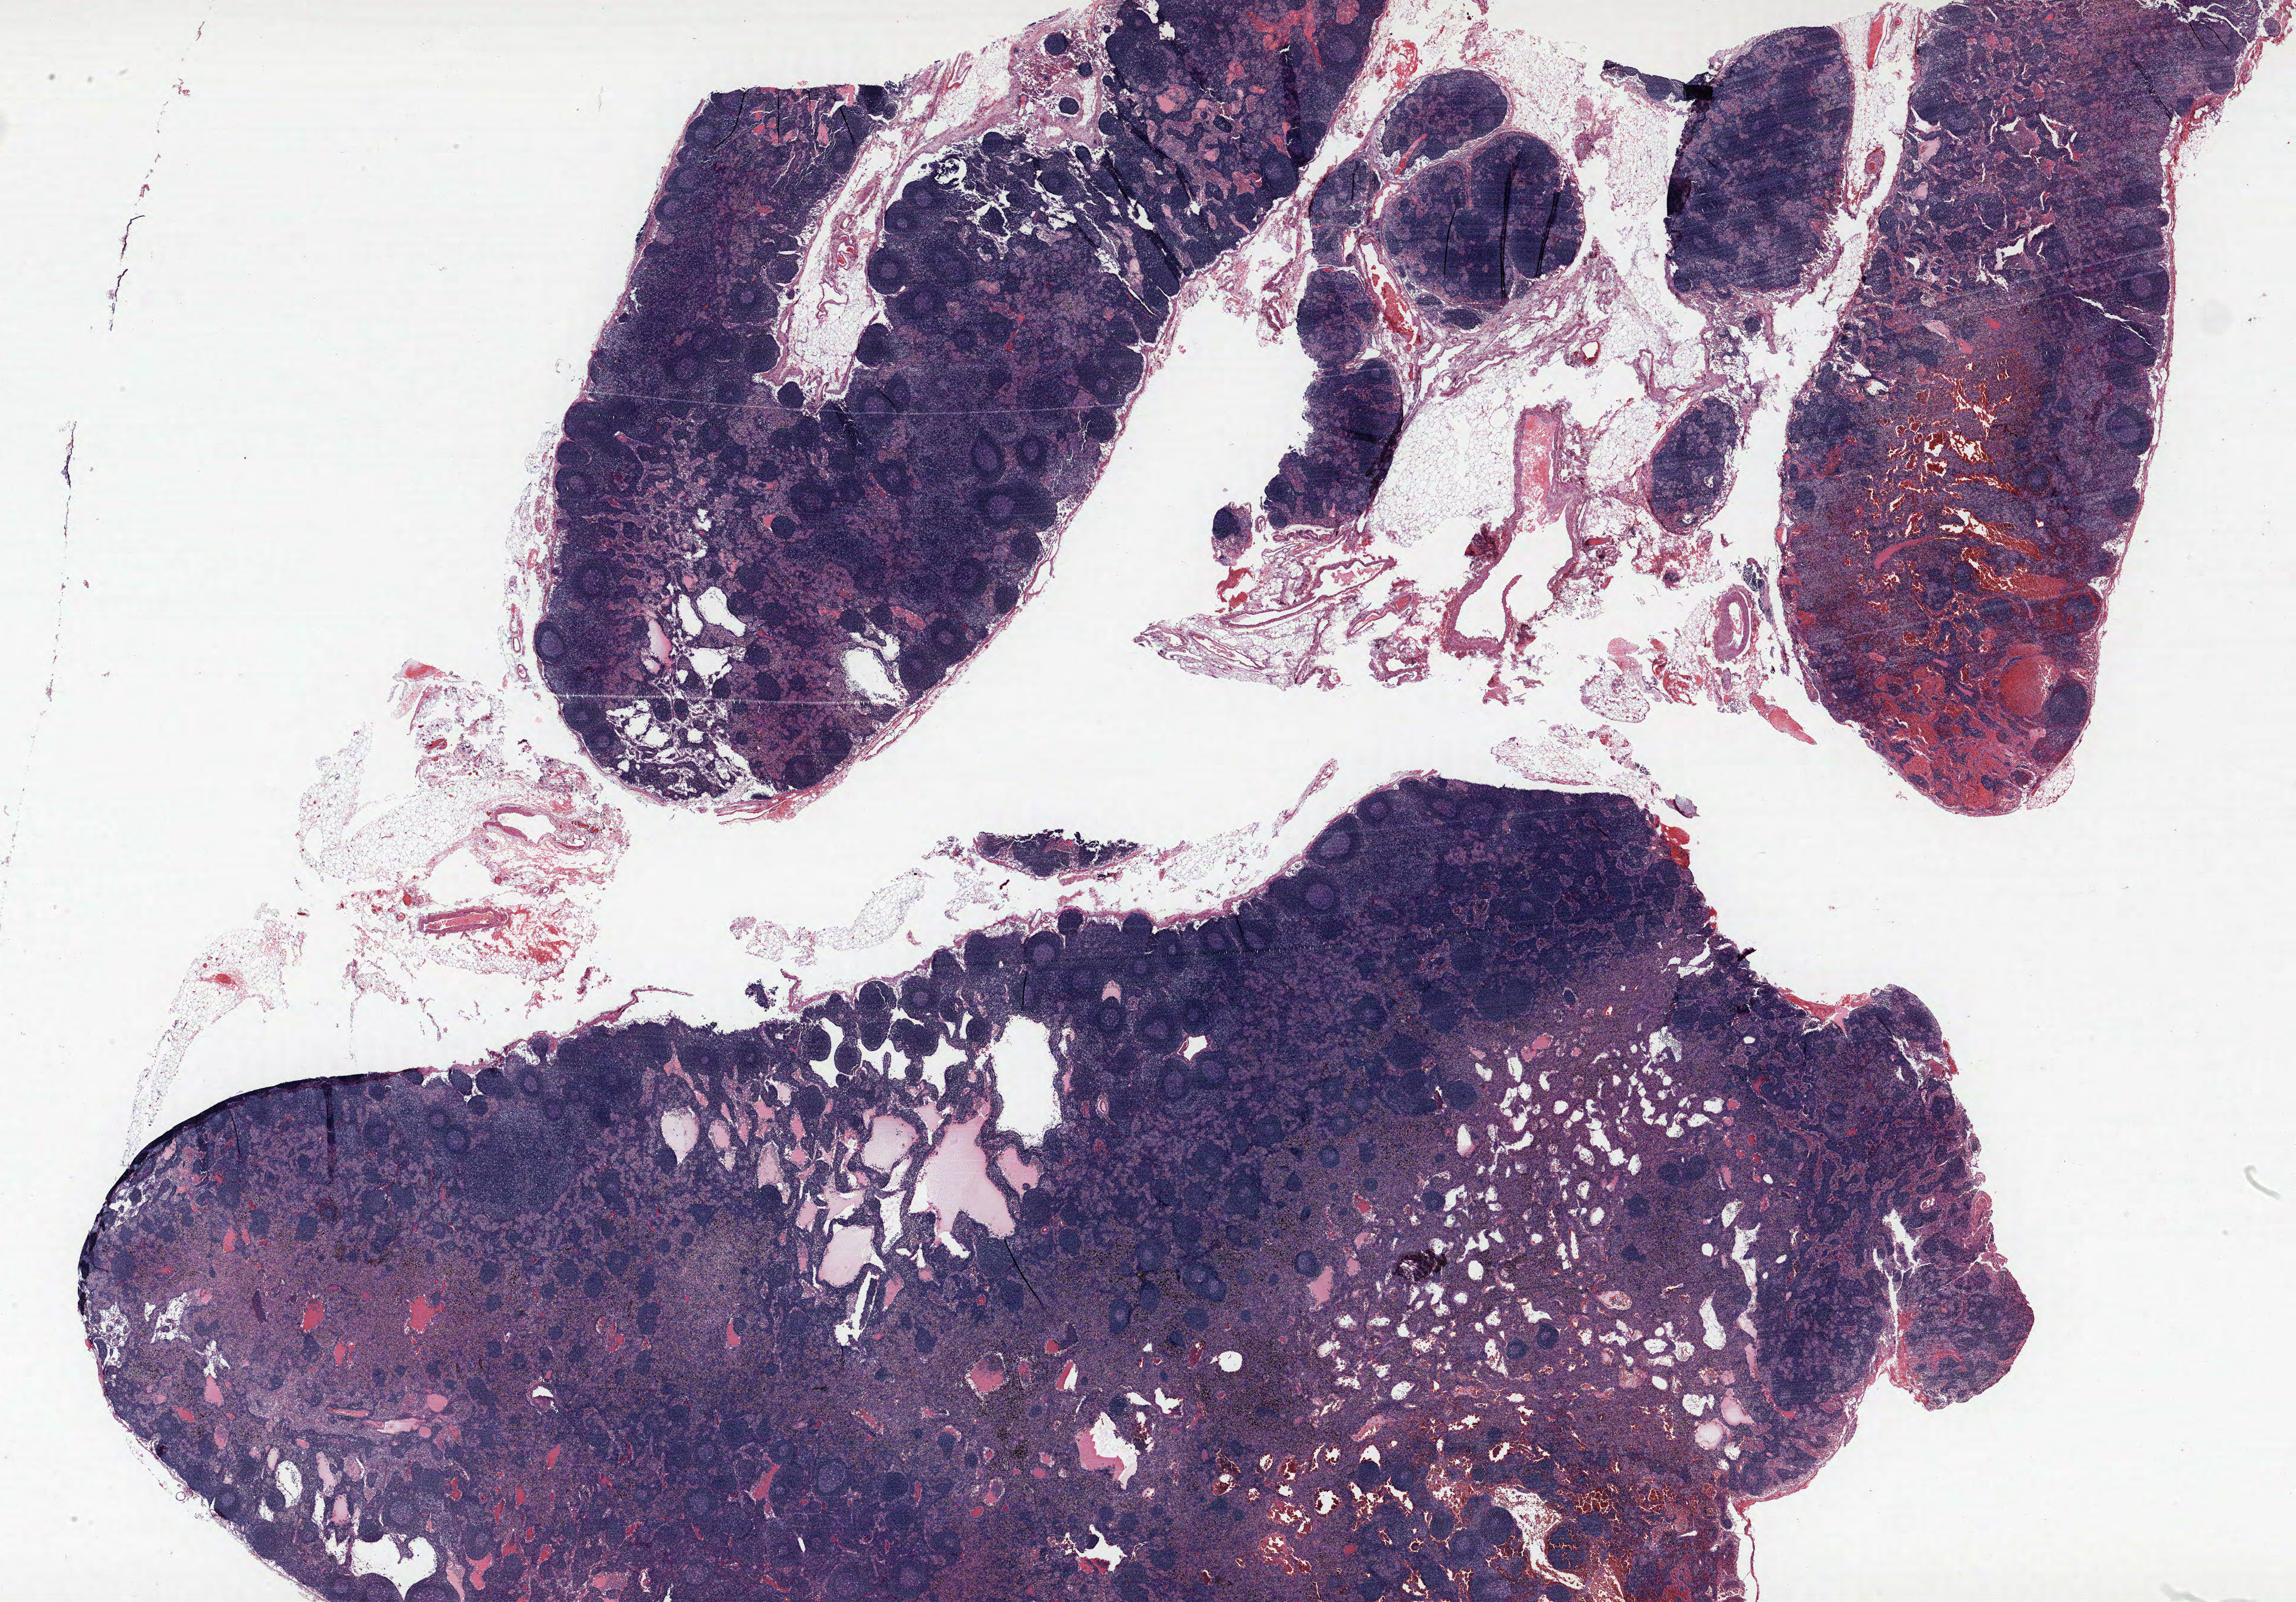
Whole-slide histology image, H&E — low-resolution overview of the scanned area, about 30.7 x 21.4 mm (acquisition: 40x scan); FFPE section; lung. Male, age 66 at enrolment. Current smoker at enrolment. Grade: moderately differentiated (G2).
* primary tumour location (clinical record): right upper lobe
* stage (AJCC 6th edition): IIB
* participant's lung-cancer diagnosis: Squamous cell carcinoma, NOS (ICD-O-3 8070/3)
* tumour size (pathology): 39 mm